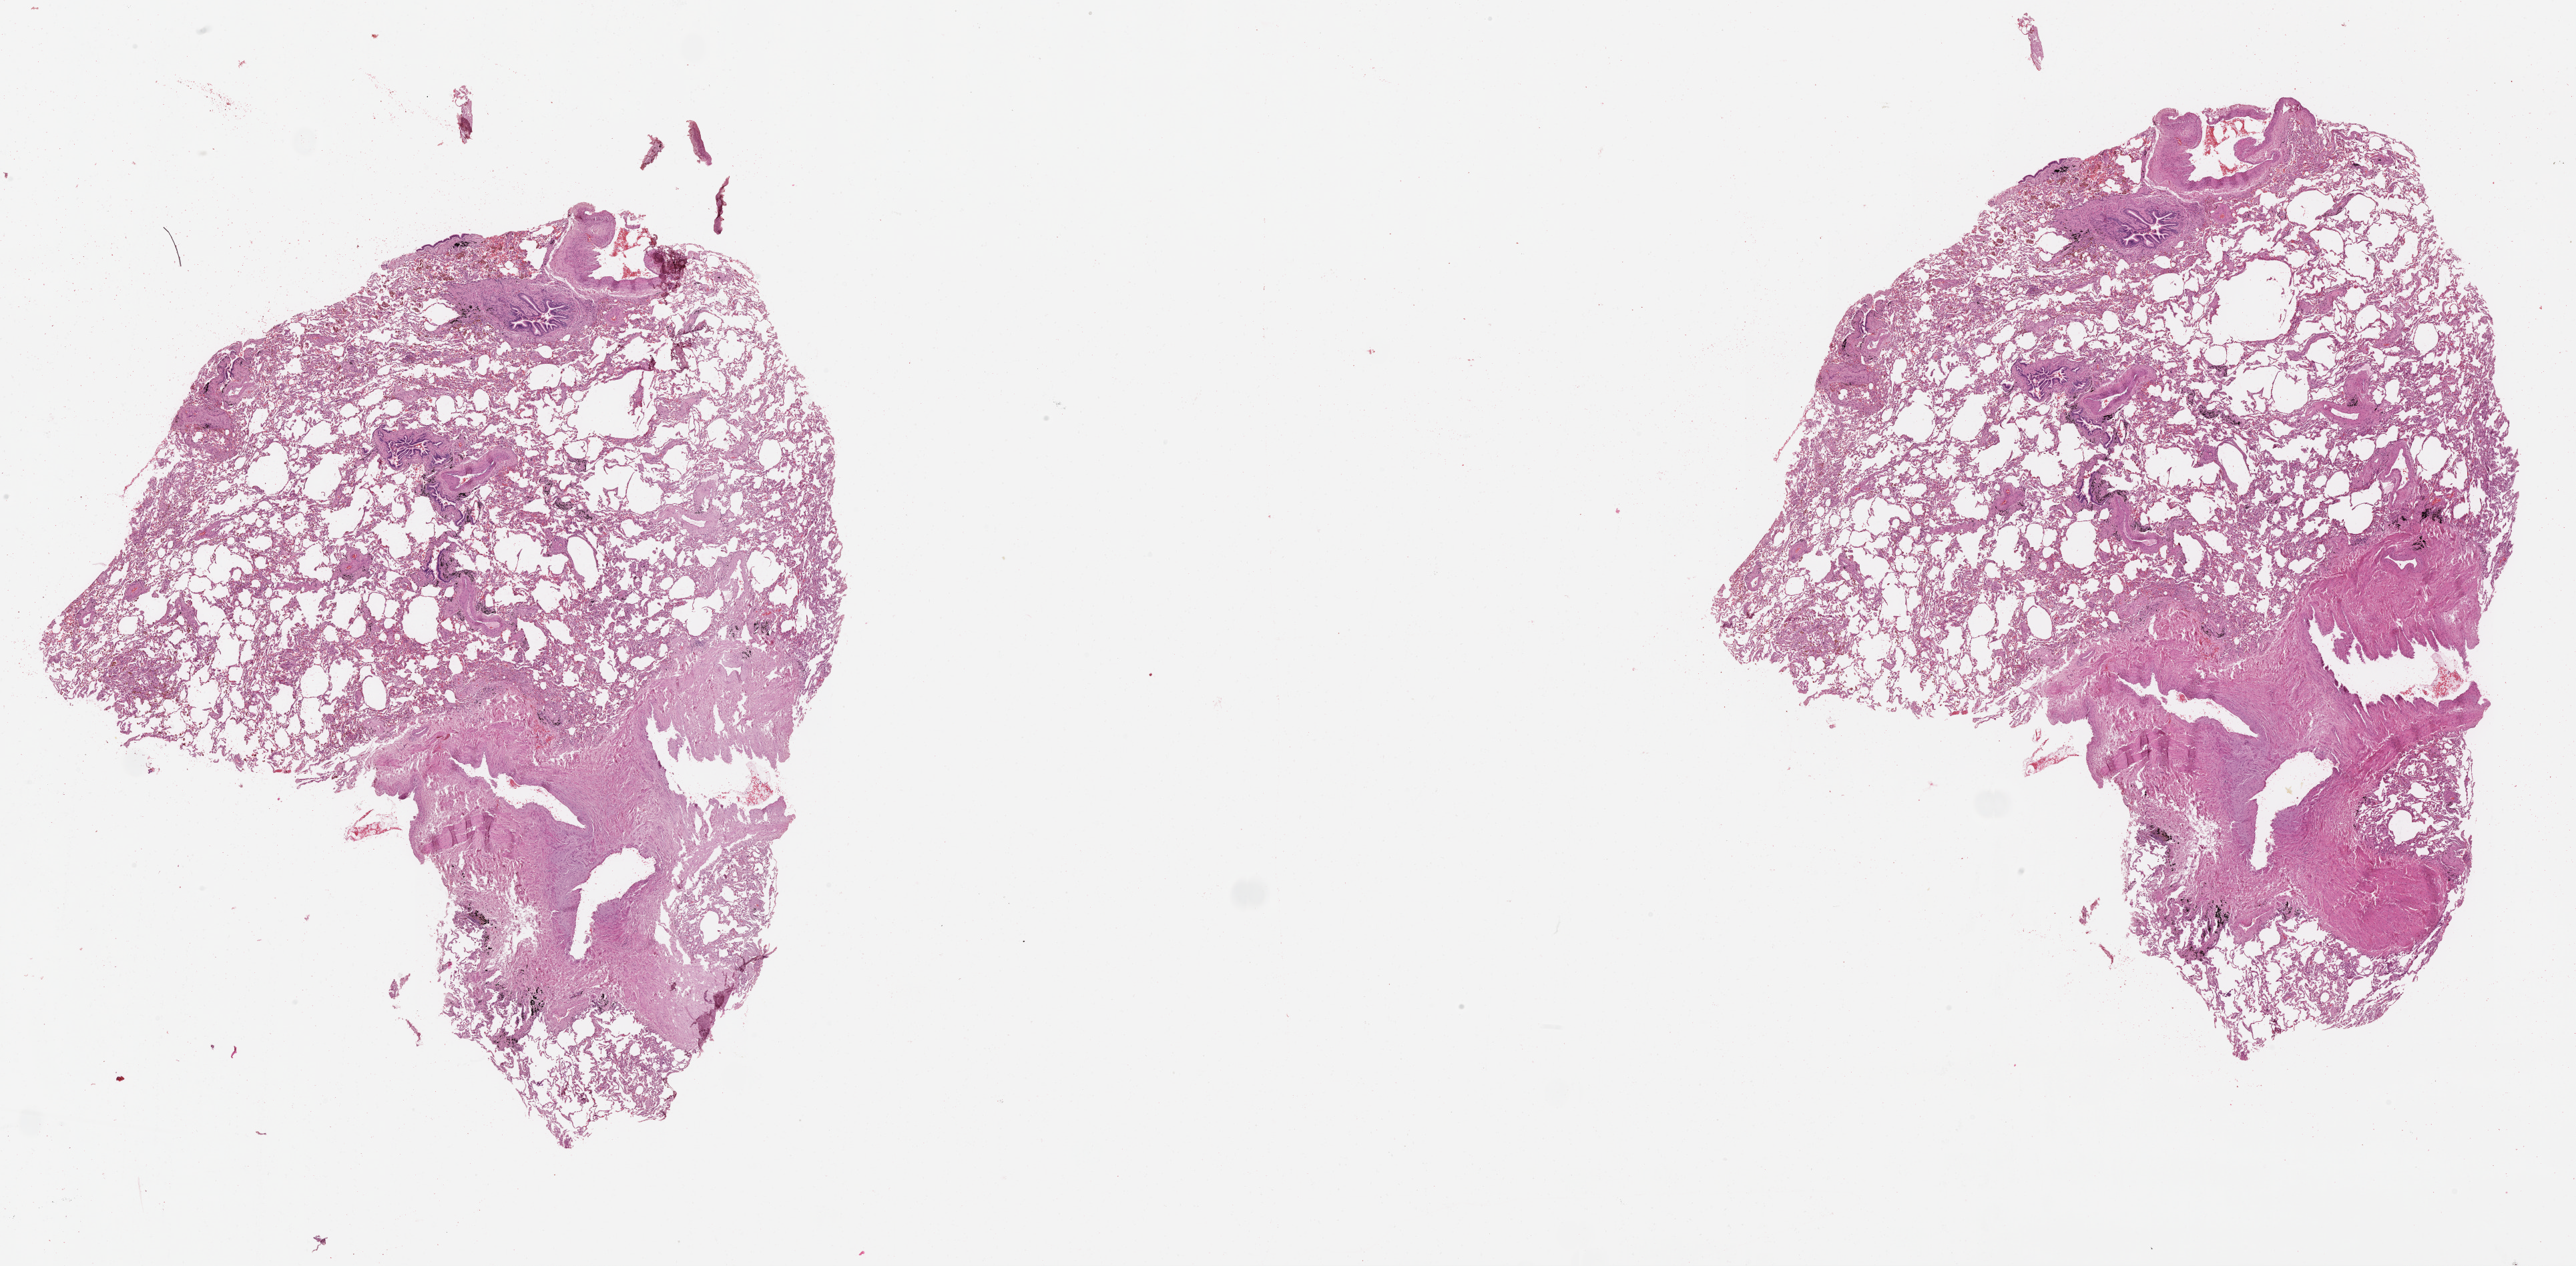
Whole-slide histology image, H&E-stained — shown as a low-resolution overview of the whole scanned area (about 31.1 x 15.3 mm, acquisition: 20x scan). Normal (non-tumour) tissue sample, lung. Male, 77 y/o.
This section: normal (non-tumour) tissue from the same patient. Patient diagnosis (cohort enrolment): squamous cell carcinoma (lung).